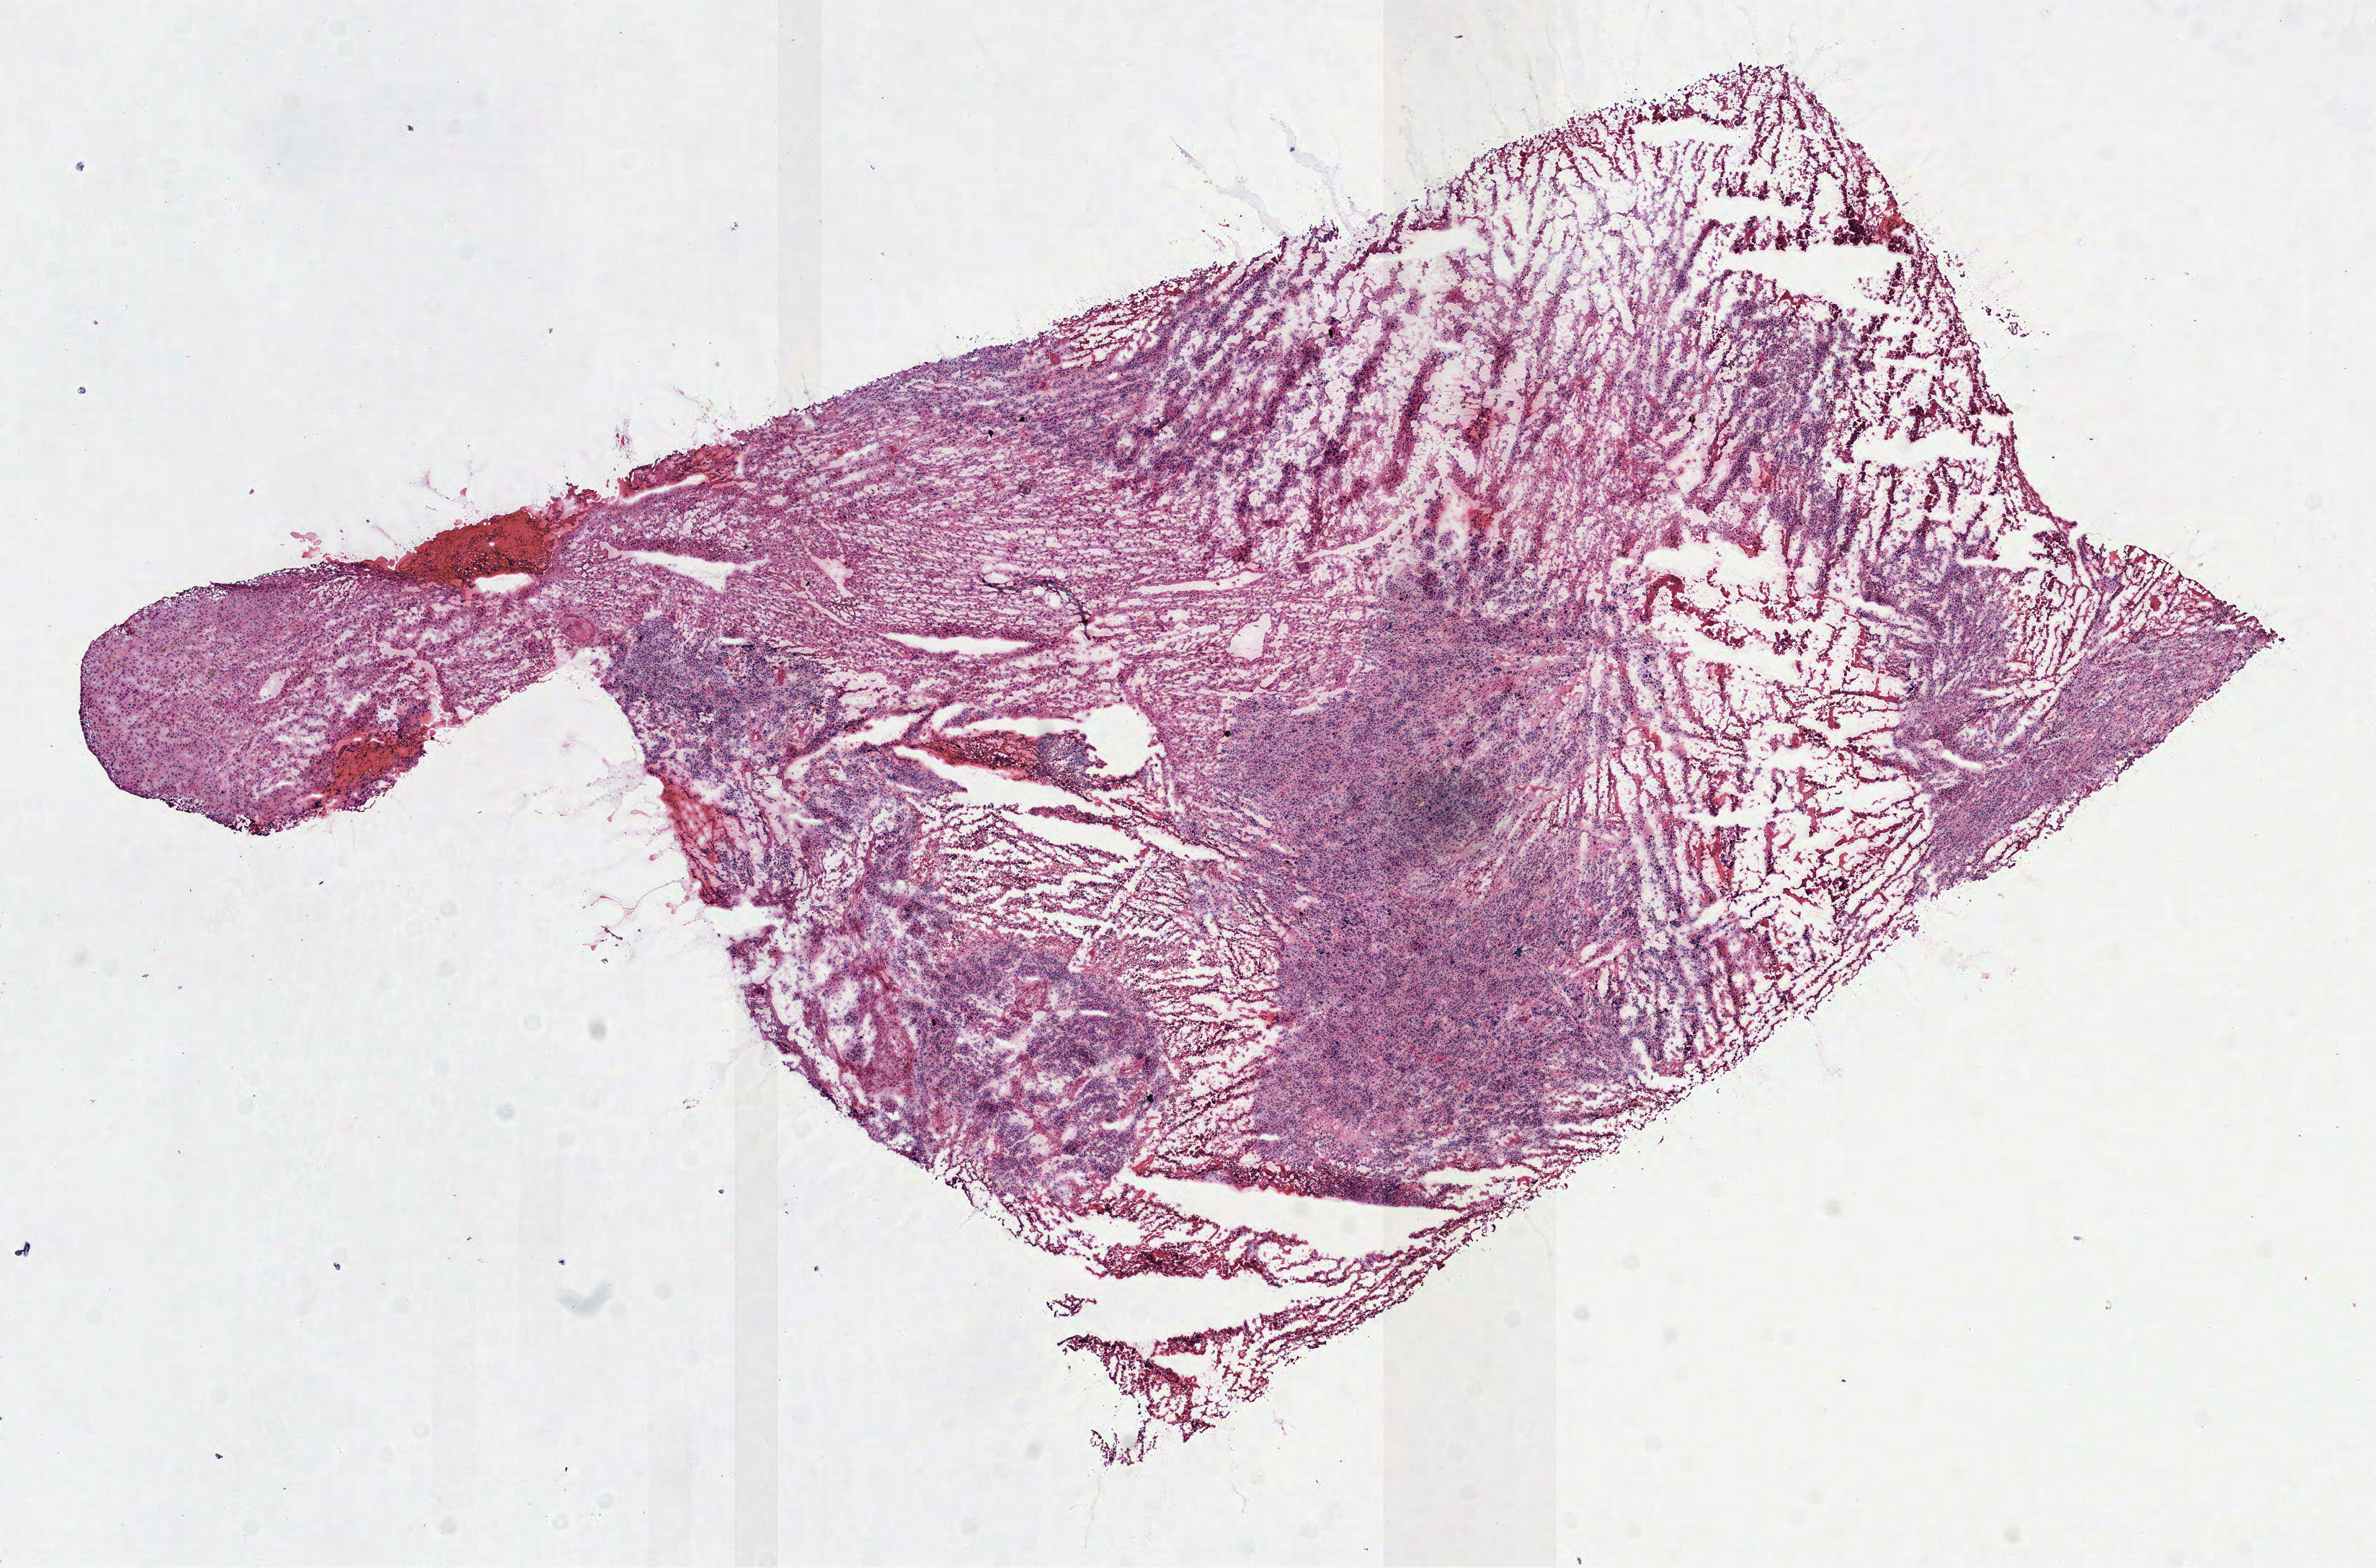
H&E whole-slide image, whole scanned area (about 13.3 x 8.8 mm) shown as a low-resolution overview. Frozen section from the top of the tissue portion. Primary tumour sample from the brain. Female patient; age at initial diagnosis 71 years. Slide review estimates, as recorded: tumour cells 85%, tumour nuclei 85%, normal cells 0%, stromal cells 0%, necrosis 15%.
Histologic diagnosis: Glioblastoma.